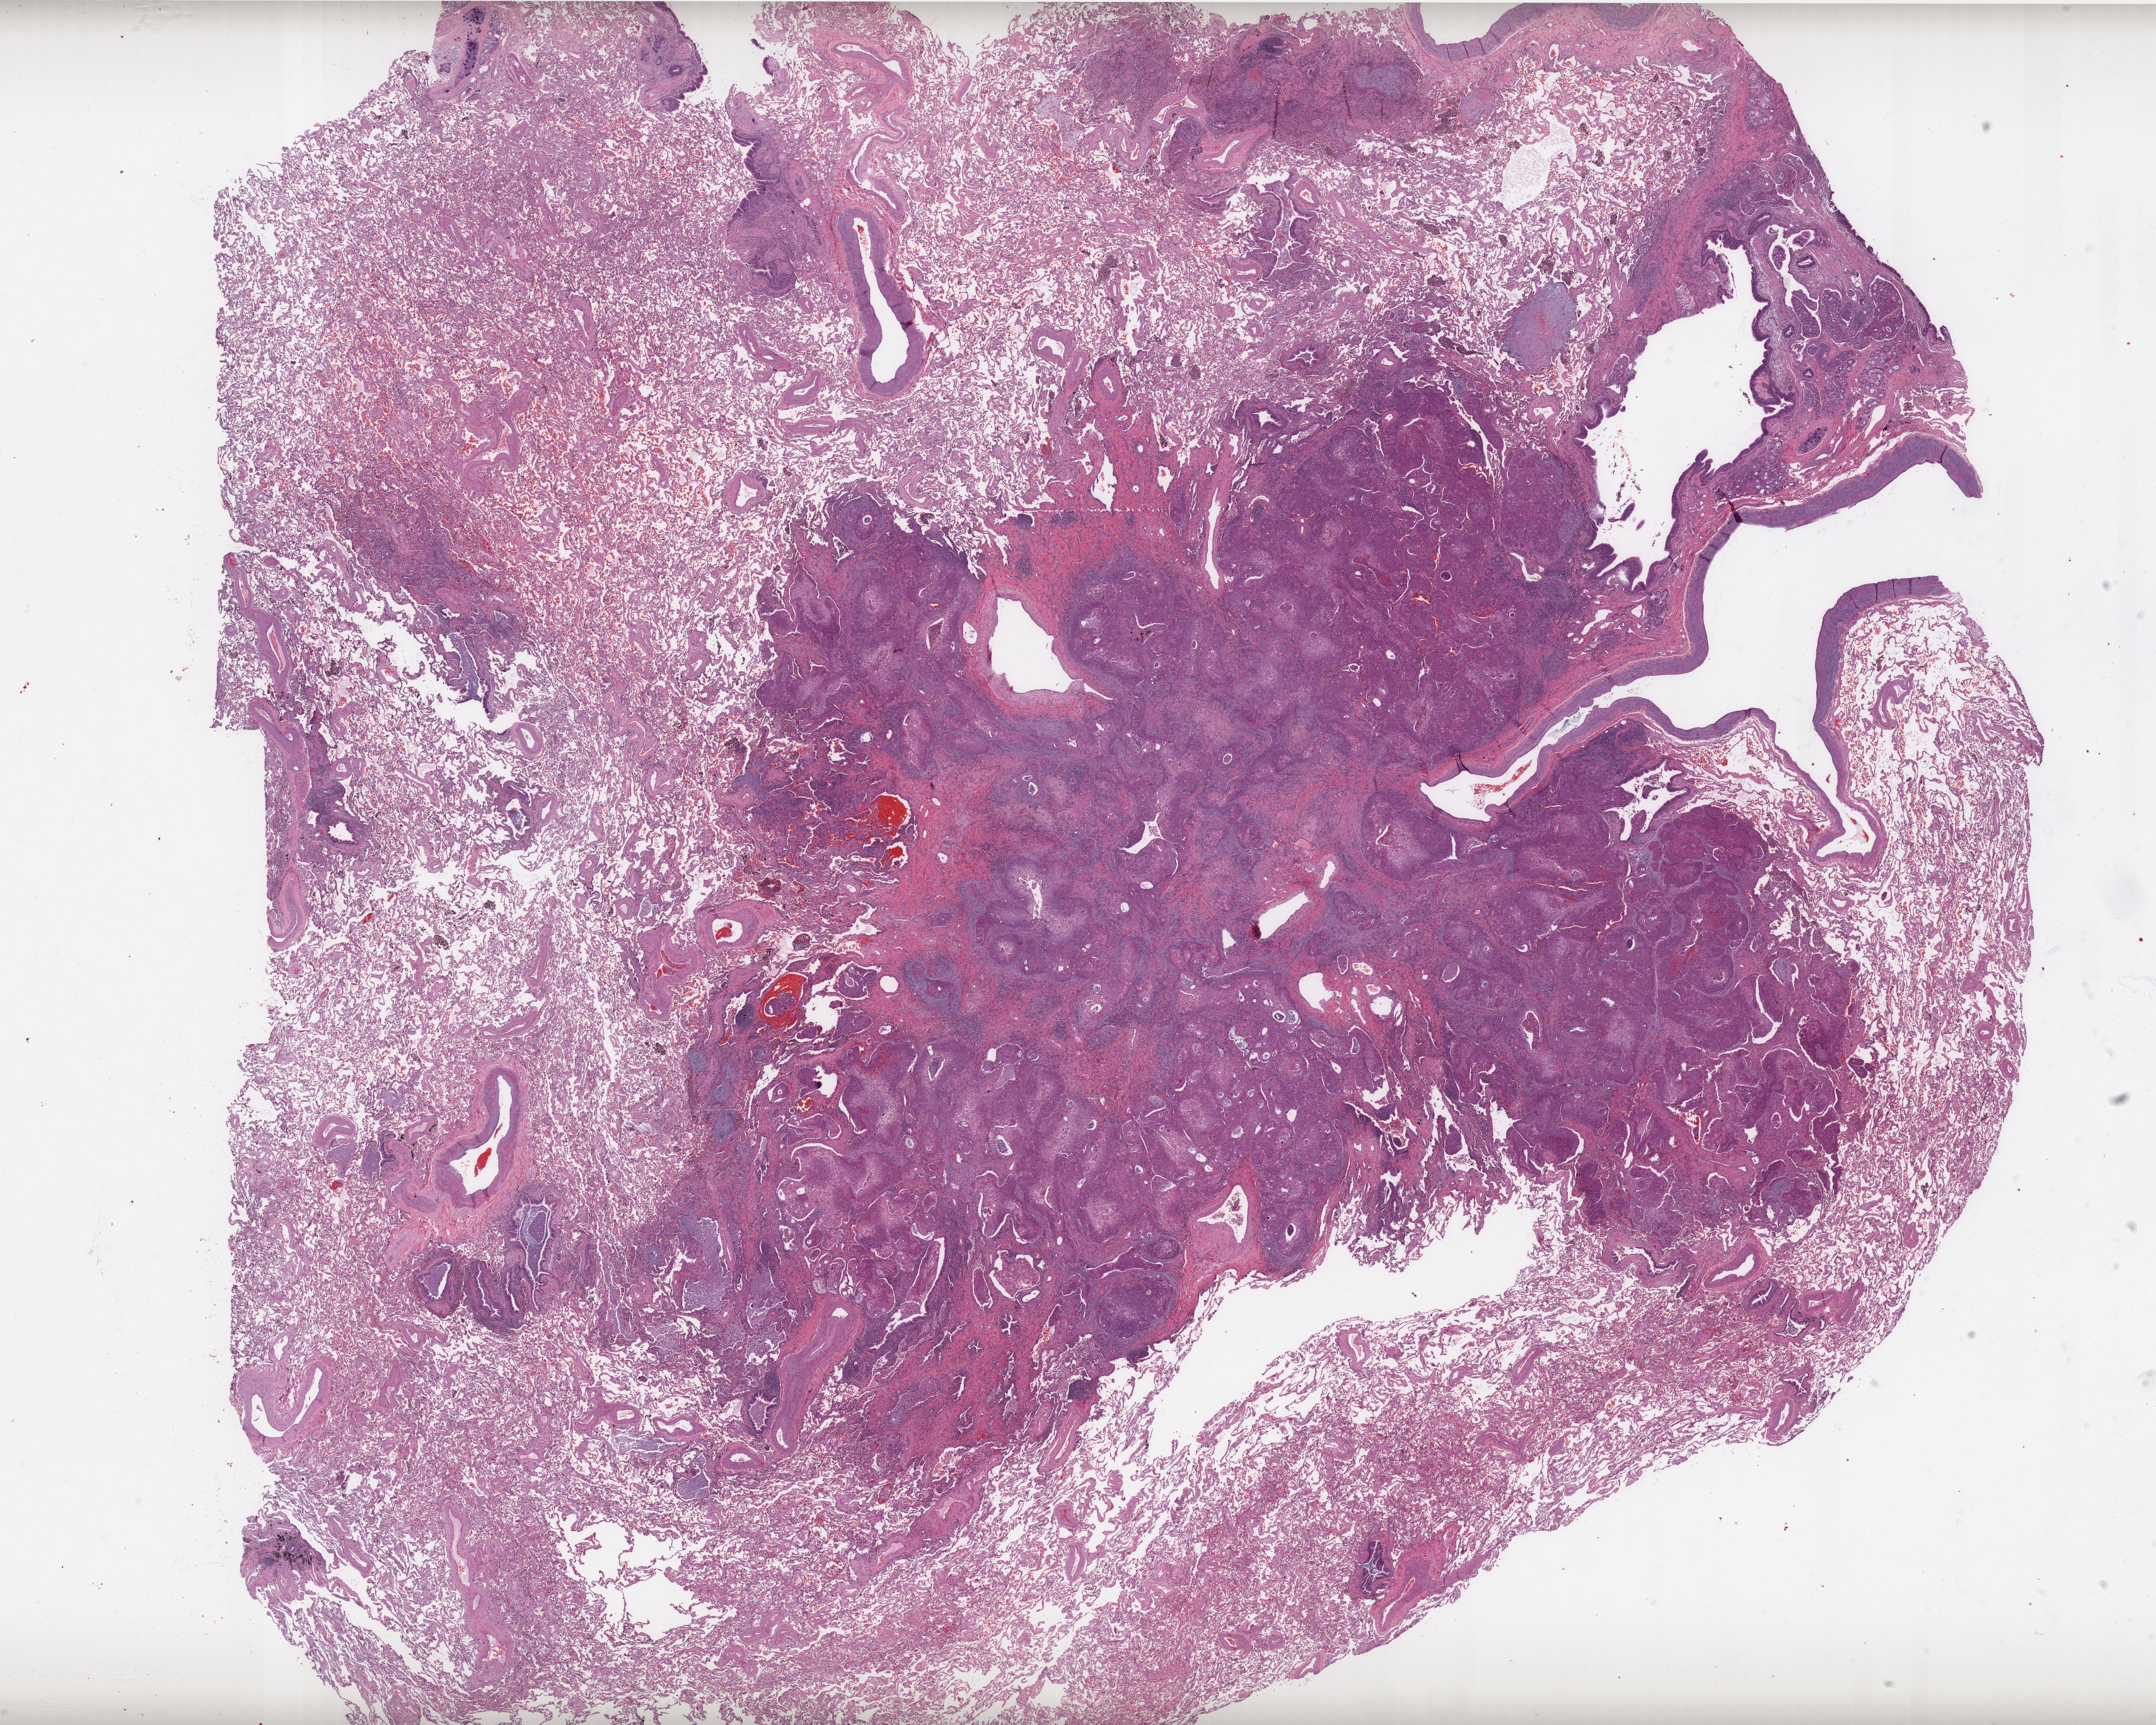
H&E-stained whole-slide image, a low-resolution overview of the entire scanned area, about 27.4 x 21.9 mm, formalin-fixed paraffin-embedded (FFPE) diagnostic section, lung, primary tumour sample. Patient: female, age at initial diagnosis 75 years.
Laterality: right. AJCC pathologic stage: IIA (7th edition). Histologic diagnosis: Squamous cell carcinoma, NOS (lower lobe, lung).